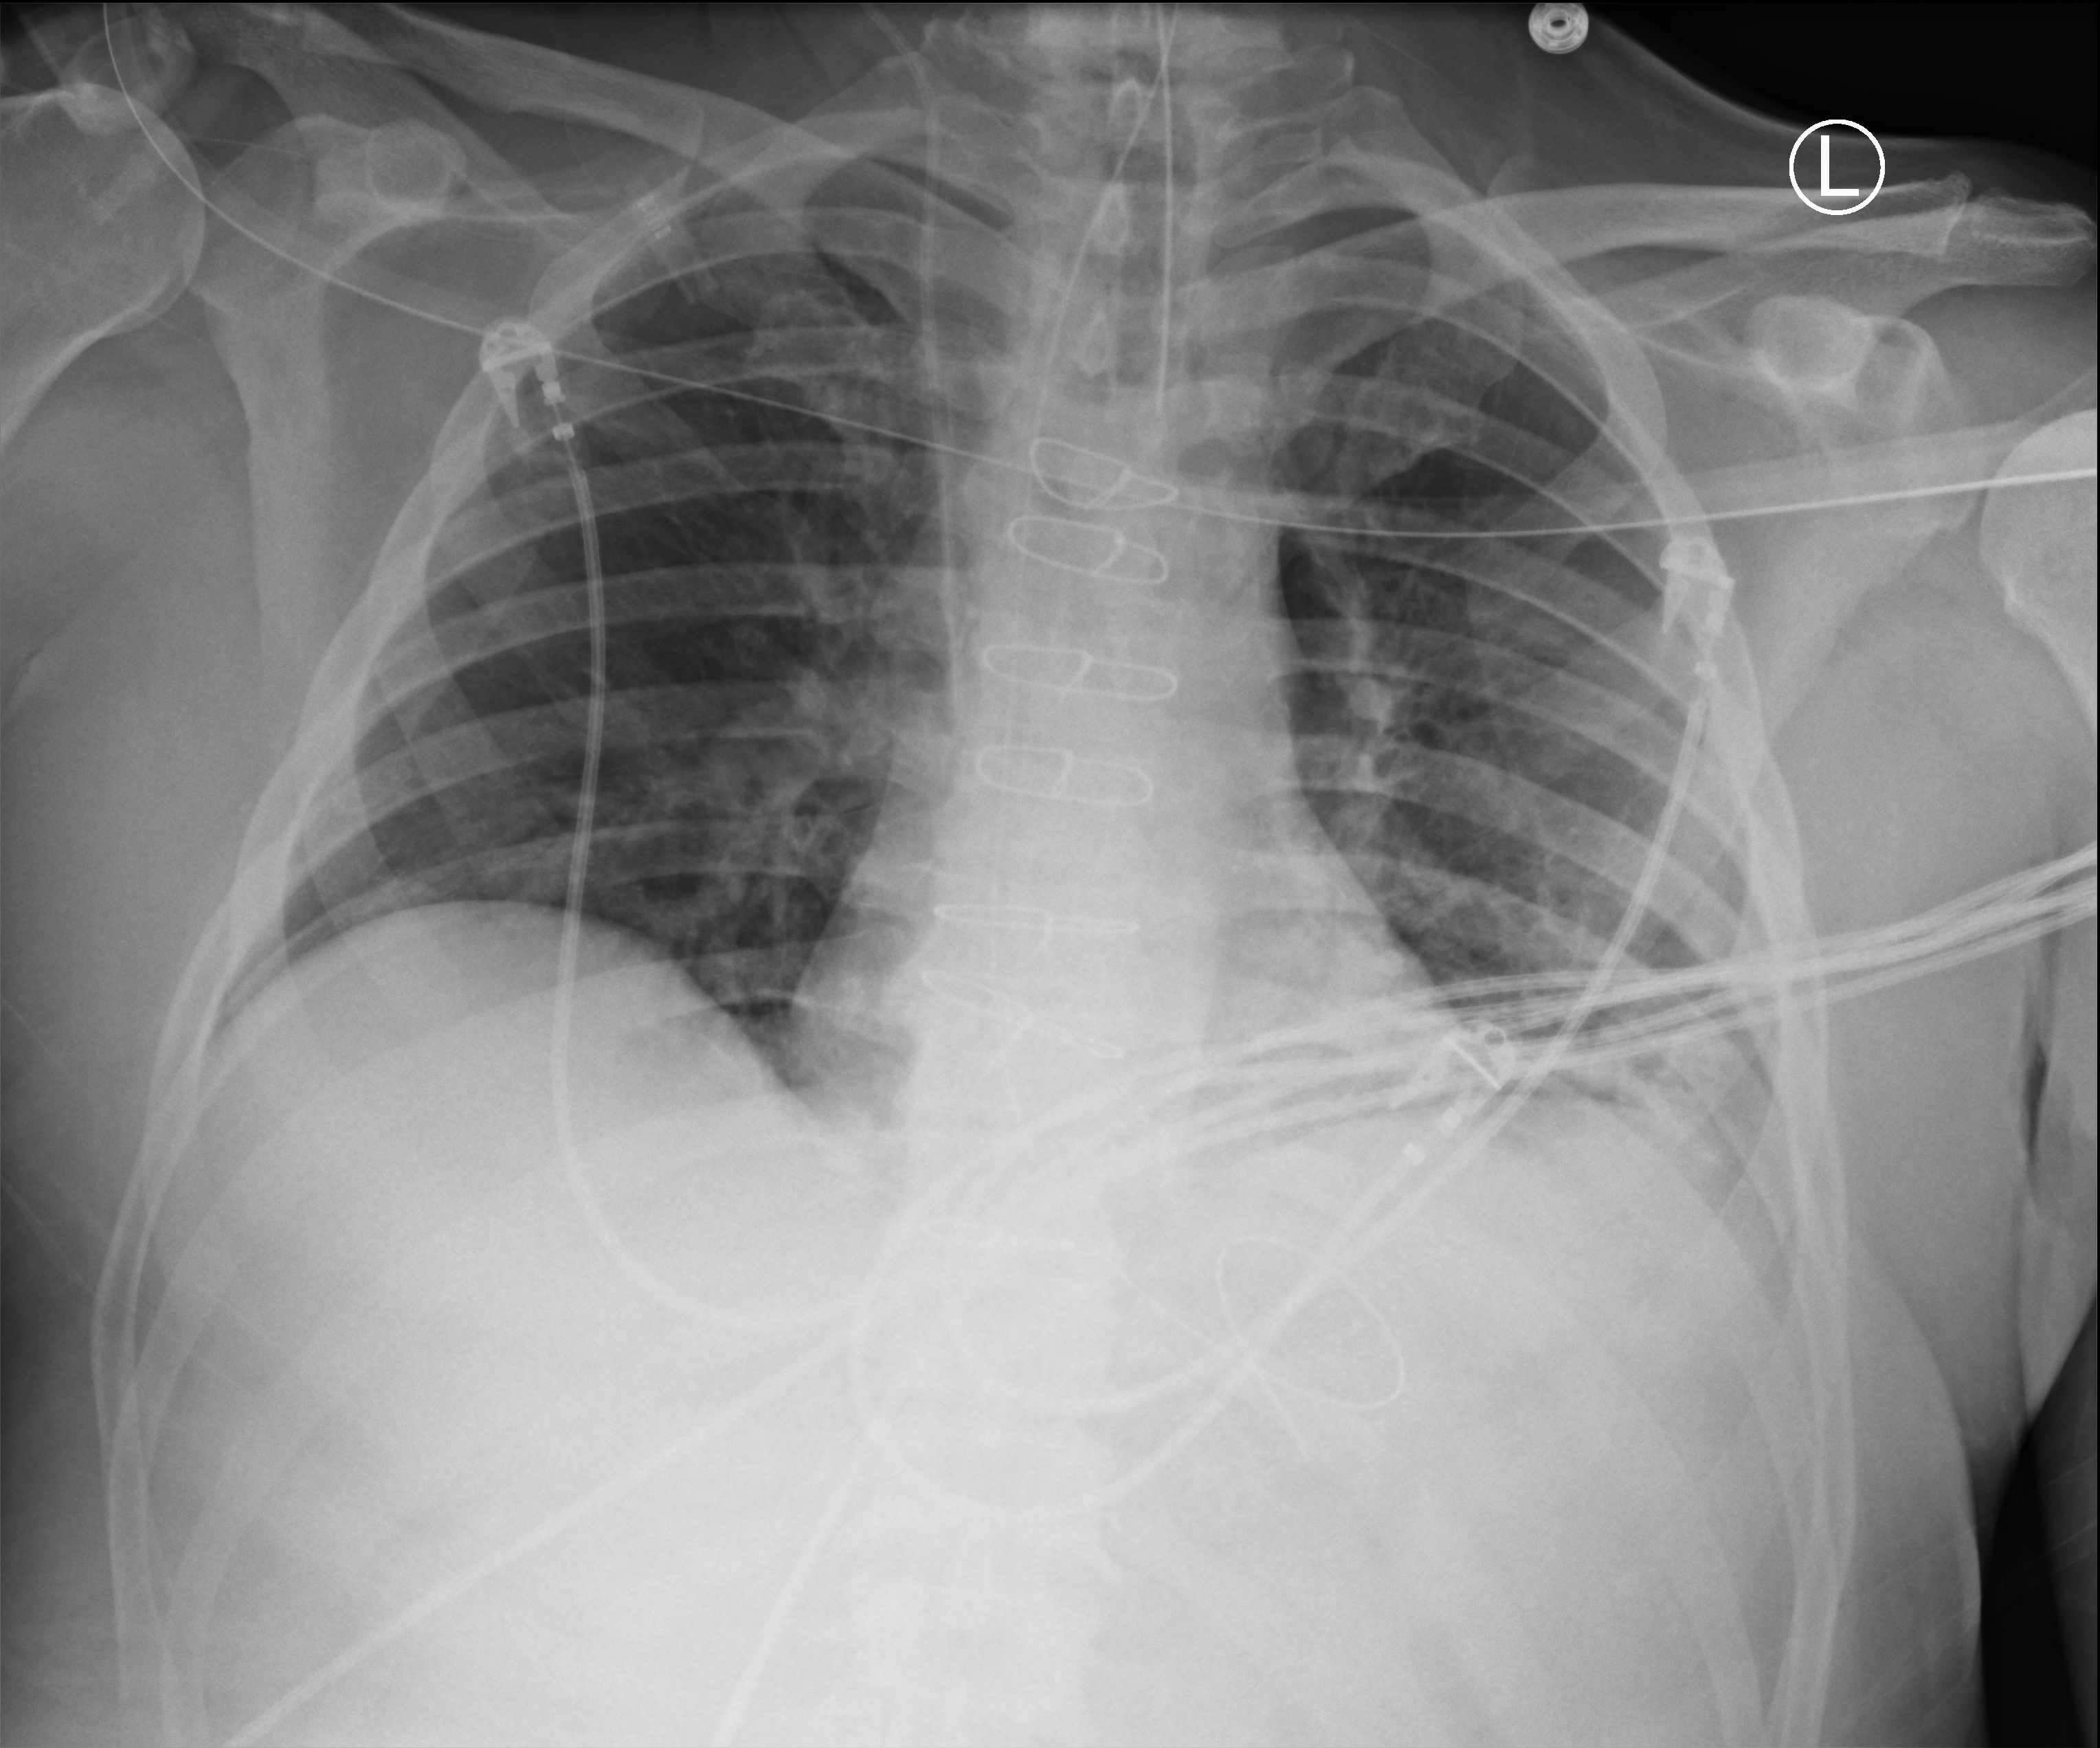
Chest X-ray (portable); anteroposterior (AP) projection. Patient hospitalised with COVID-19; male, aged 60–74 years.
From the hospital-stay record, not from the radiograph (when in the stay this image was taken is not recorded):
- hypertension (admission record): yes